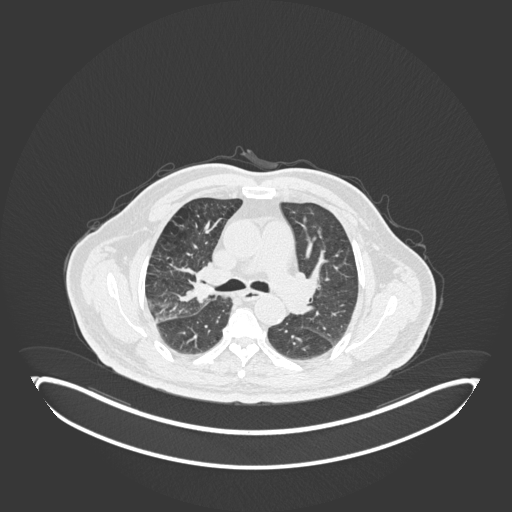
Chest CT, one axial slice; slice 111 of 247 in the series (ordered by position); reconstruction kernel B30f; lung window (W 1500 / L -600 HU); 512 × 512 image matrix. Male patient, age 72 years. From the clinical record (not read from this slice): clinical TNM (as recorded): T1c N0 M0.
Structures marked on this image (rectangle marked by the reading radiologist):
- lung tumour (recorded histology: squamous cell carcinoma): bounding box (x1, y1, x2, y2) in pixels: (178, 254, 217, 305)